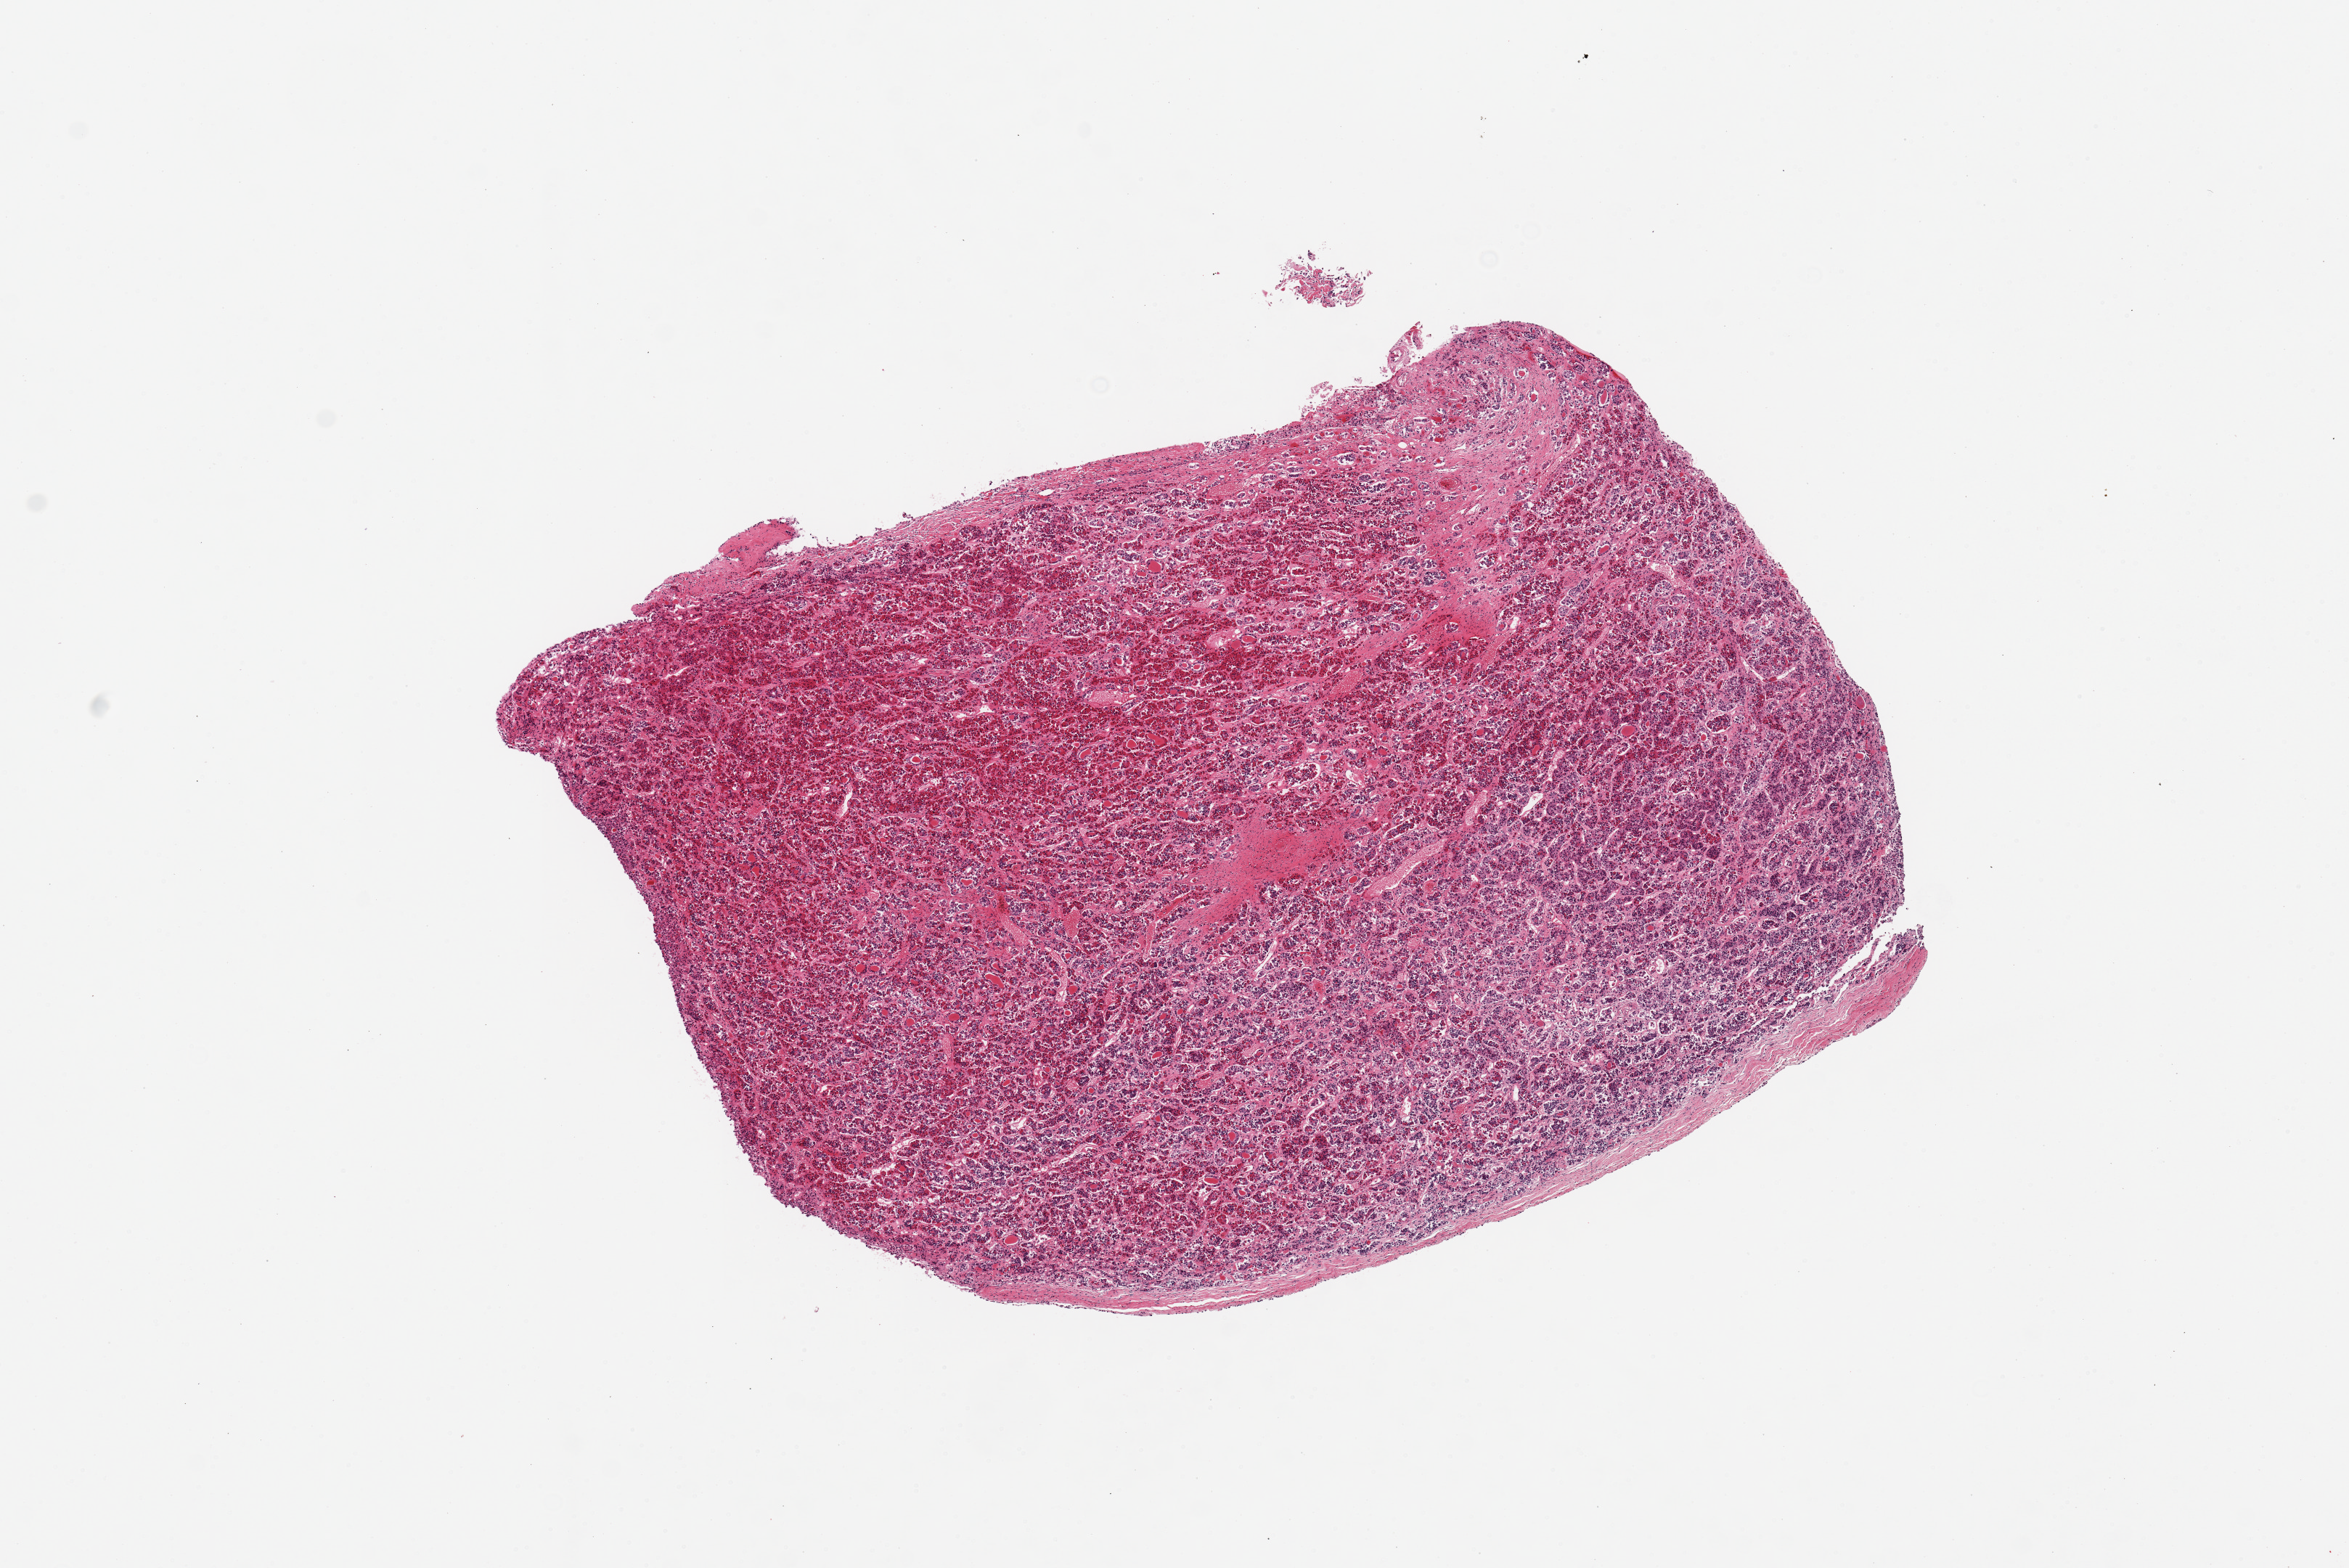
Whole-slide image, haematoxylin and eosin stain, brightfield, whole scanned area (about 12.8 x 8.5 mm, acquisition: 20x scan) shown as a low-resolution overview. PAXgene-fixed paraffin-embedded (PFPE) section. Target tissue: pituitary. Donor tissue sample. Female donor.
- review note (as recorded): 1 piece, all adenohypphysis